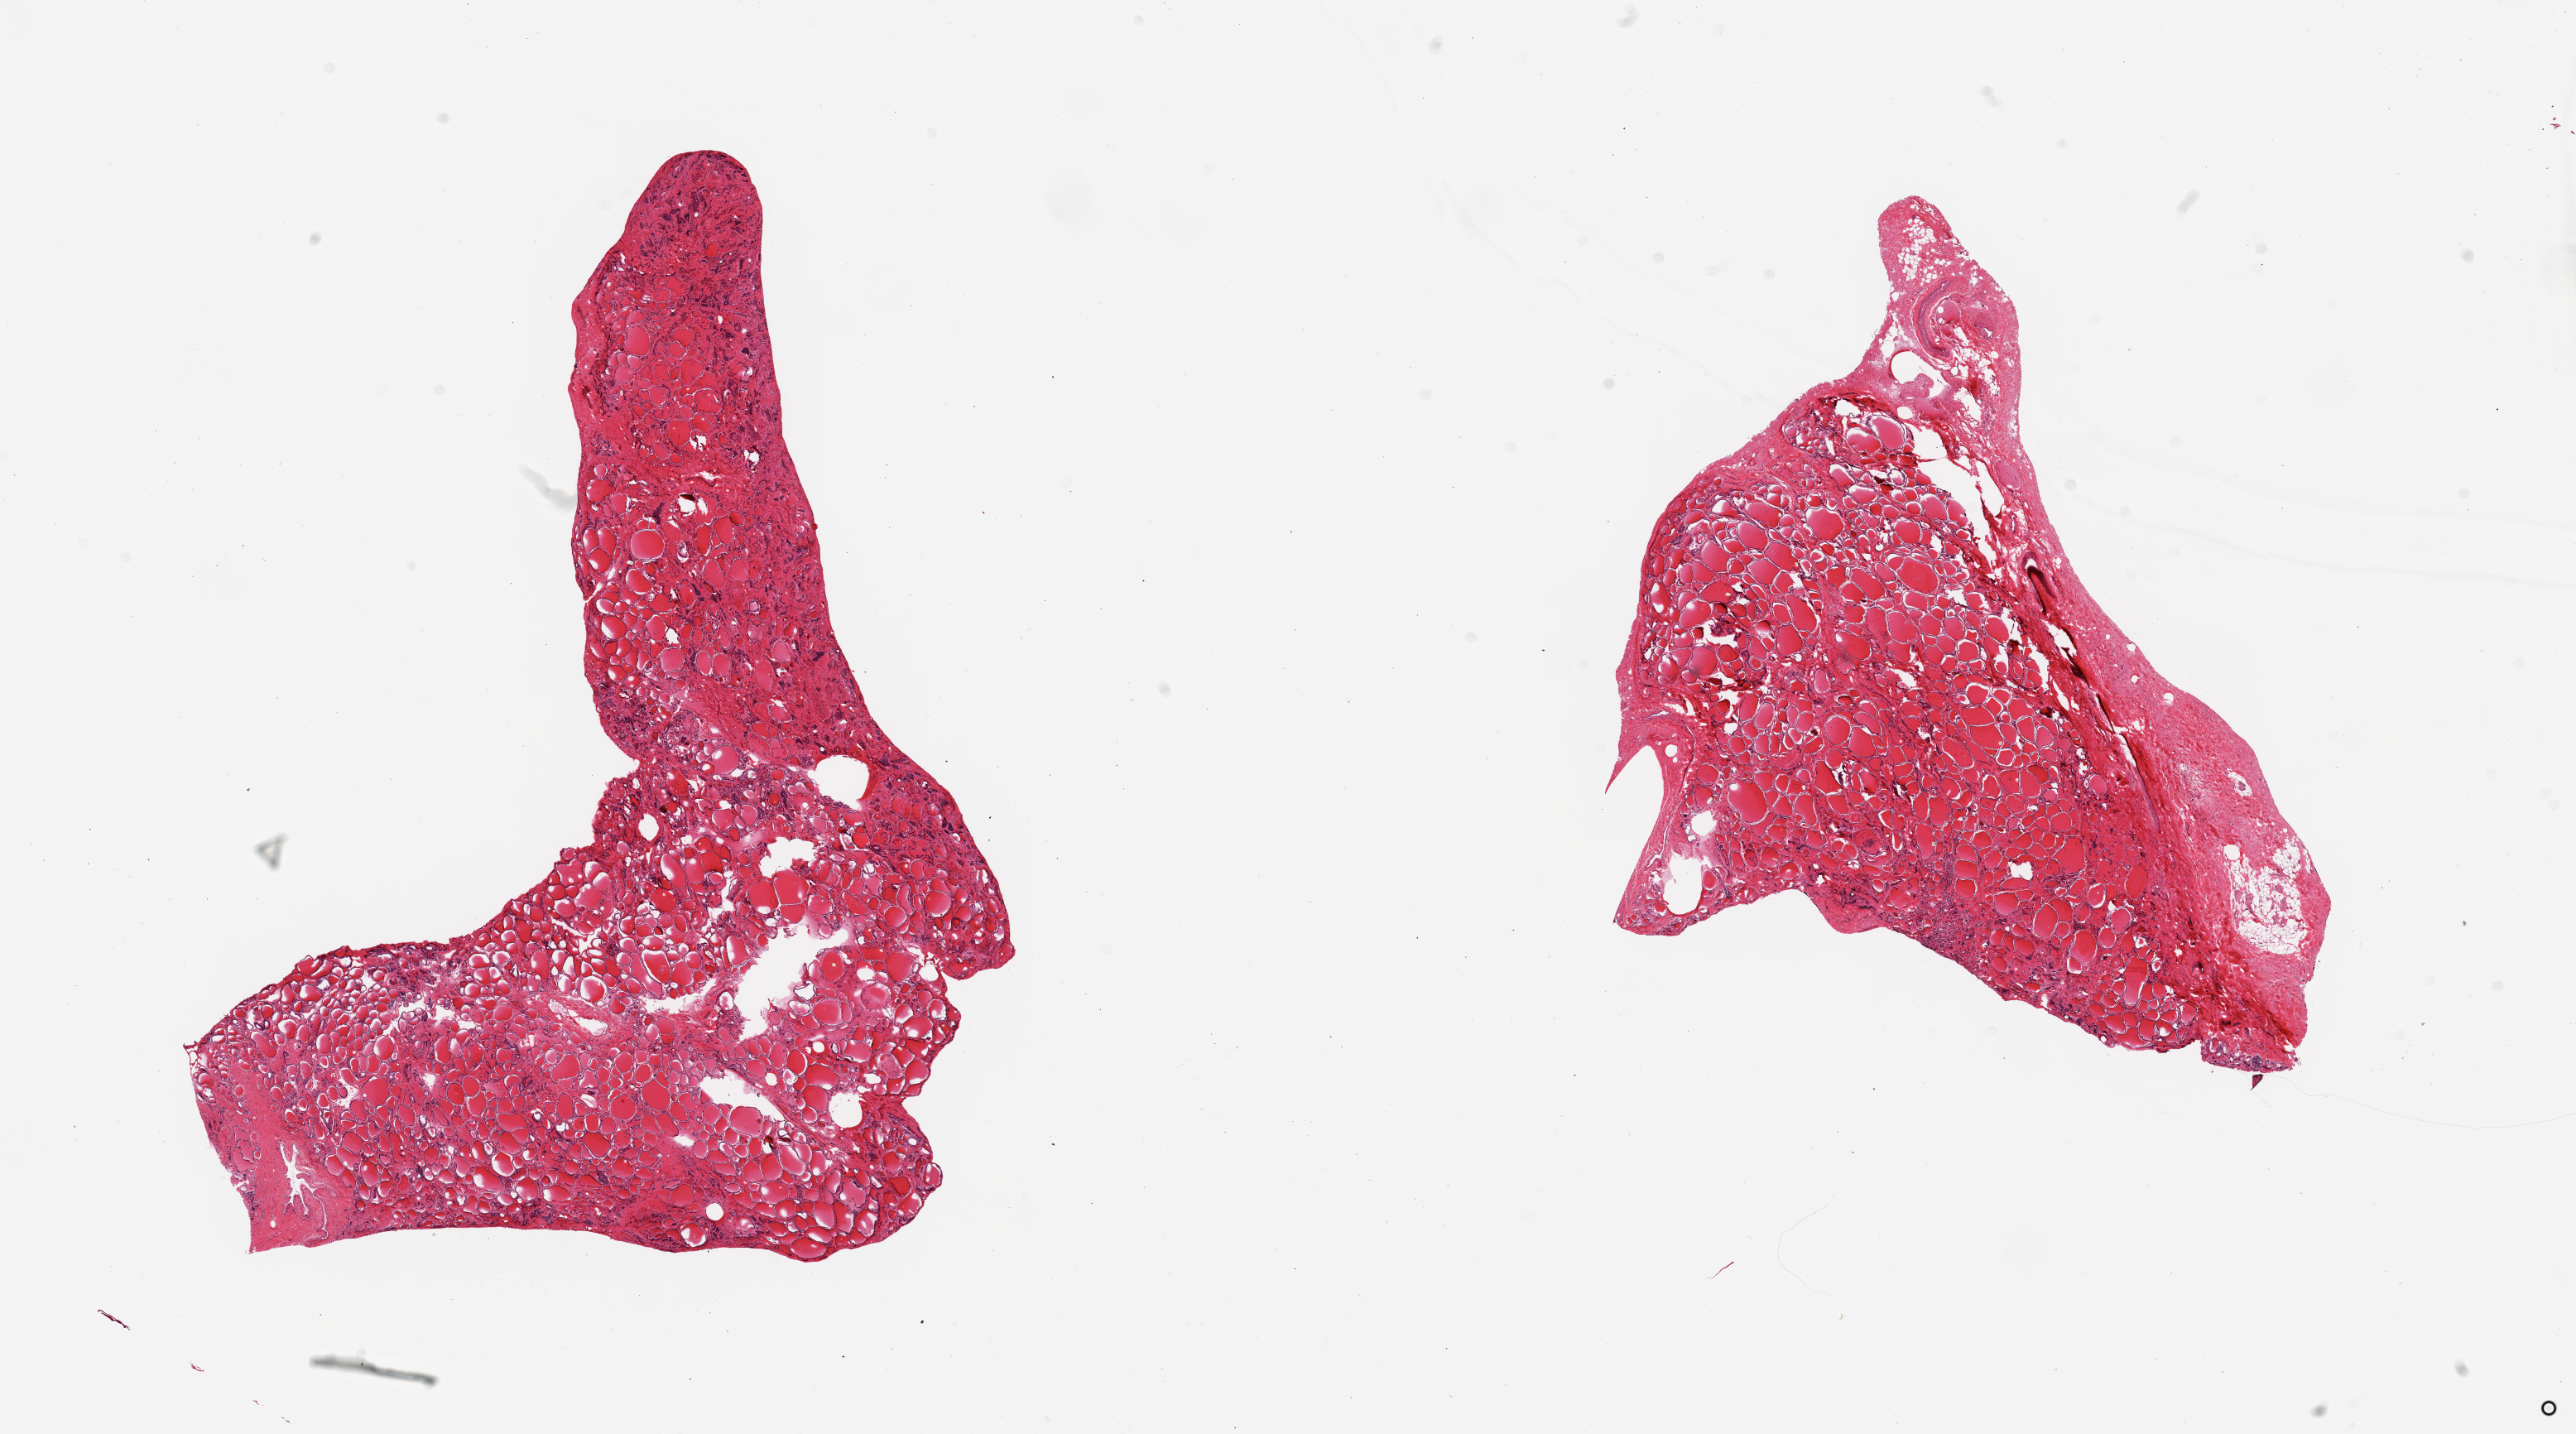
Digitized H&E-stained section, a low-resolution overview of the entire scanned area, about 24.6 x 13.7 mm. PAXgene-fixed, paraffin-embedded tissue. Sampled site (target tissue): thyroid. Tissue donor sample.
Reviewer comment on this tissue sample: 2 pieces; fibrofatty capsule up to 1mm thick on 1 piece.